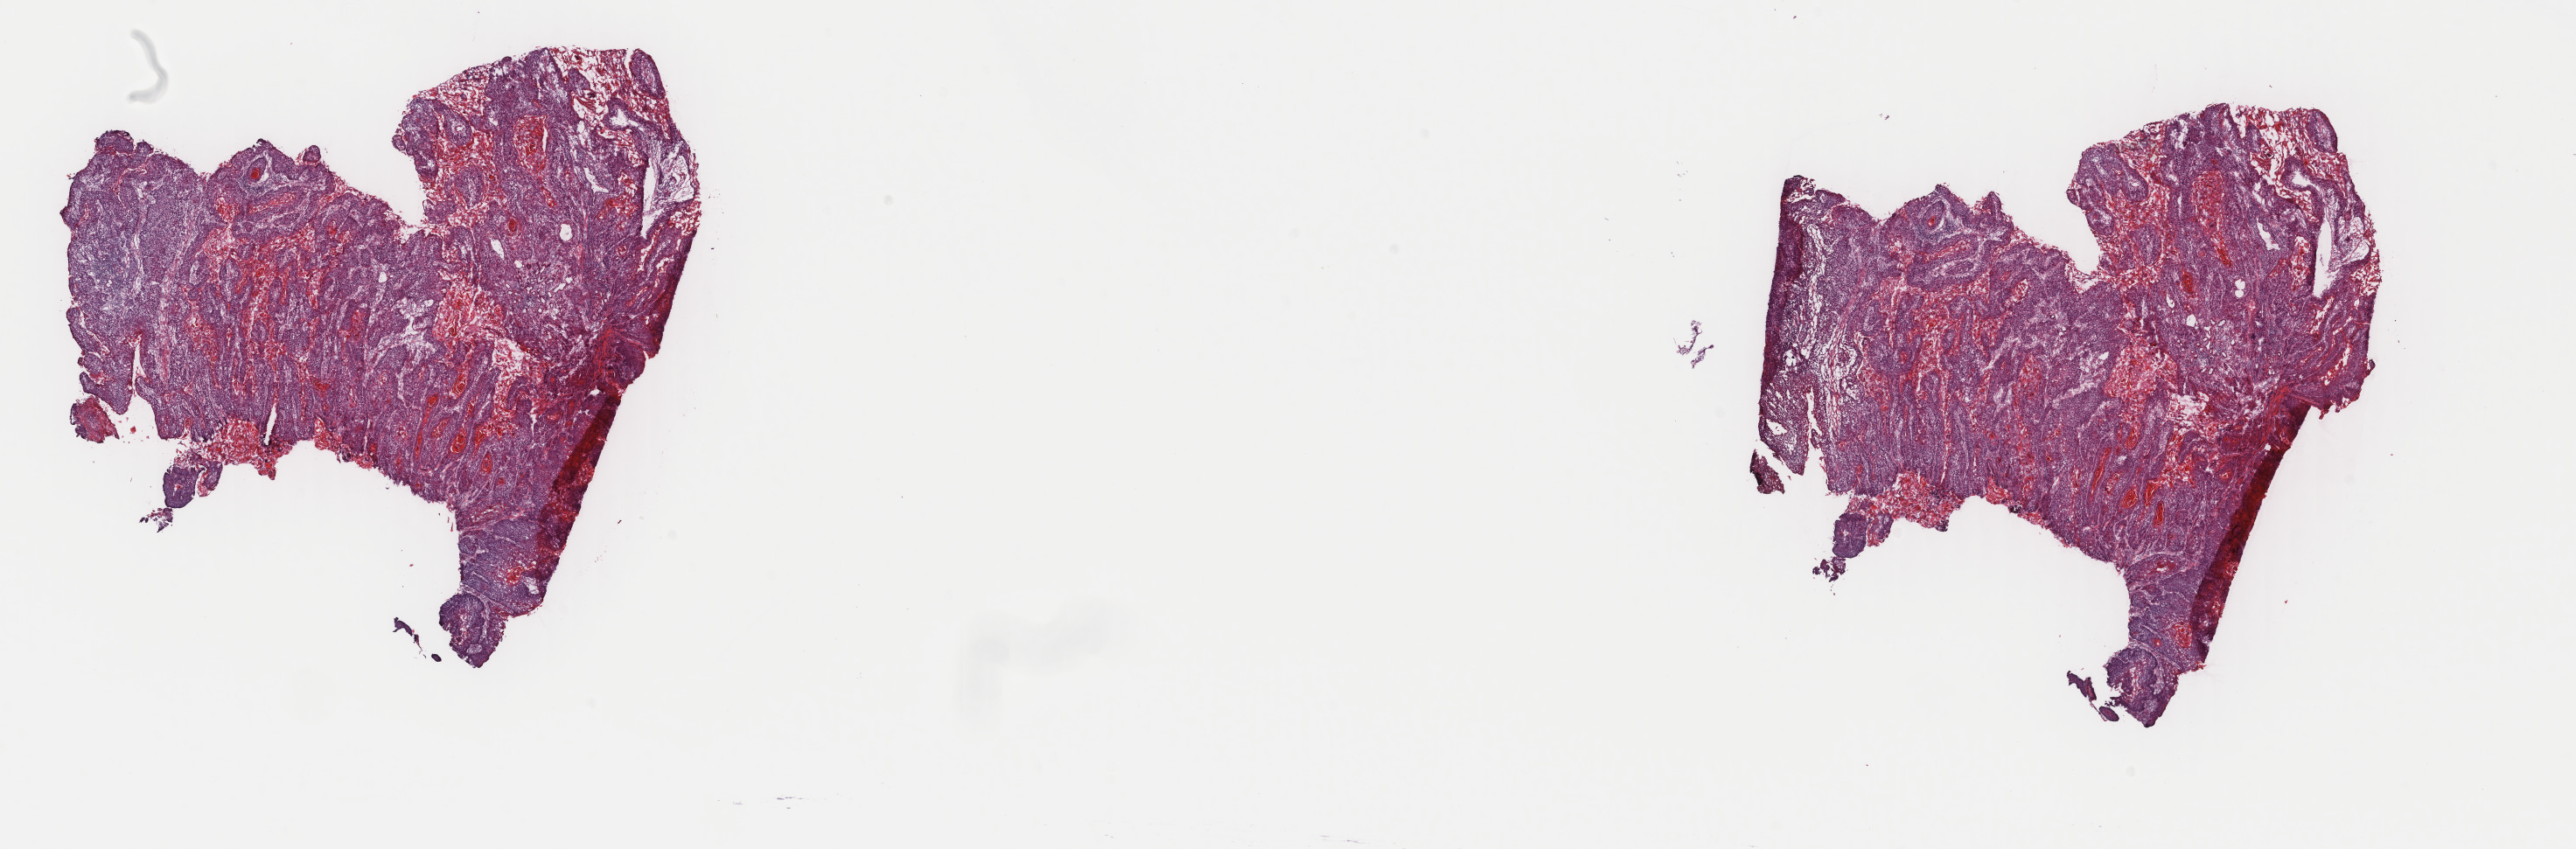
Digitized Hematoxylin and eosin (H&E) stained tissue section (whole slide), a low-resolution overview of the entire scanned area, about 23.4 x 7.7 mm (acquisition: 40x scan); frozen section from the top of the tissue portion; head and neck, primary tumour sample. Male patient; age at initial diagnosis 47 years. Histologic grade: G2 (moderately differentiated). Slide review estimates, as recorded: tumour cells 90%, tumour nuclei 85%, normal cells 0%, stromal cells 10%, necrosis 0%. Inflammatory infiltration, as recorded: lymphocyte infiltration 0%, monocyte infiltration 0%, neutrophil infiltration 0%.
AJCC pathologic stage: IVA (7th edition). Diagnosis: Squamous cell carcinoma, keratinizing, NOS (larynx, NOS).